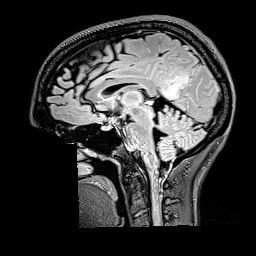
Brain MRI from a brain-tumour surgery series, one sagittal slice. Position 89 of 176 along the scan axis. T2 FLAIR. 256 × 256 image matrix, field of view 256 × 256 mm. Case-level facts recorded for this patient, not image findings: histopathology: Oligodendroglioma; WHO grade: 2; IDH mutation: yes.
Structures marked on this image (outlined manually by an expert reader):
- tumour: bounding box (x1, y1, x2, y2) in pixels: (161, 73, 190, 99)